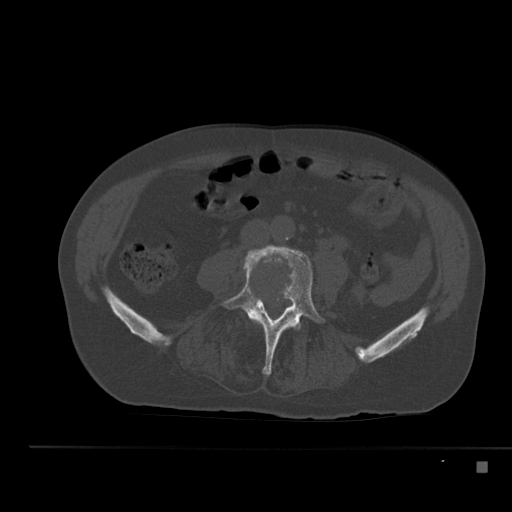
CT including the spine, one axial slice; position 143 of 517 along the scan axis; reconstruction kernel Br40s; 120 kVp; bone window (W 1800 / L 400 HU); 1.5 mm slice thickness; 512 × 512 image matrix, field of view 408 × 408 mm. Patient: male, 70 years. From the clinical record (not read from this slice): primary cancer: renal.
Annotated regions visible in this slice (semi-automatic segmentation, software-assisted and operator-edited):
- L4 vertebra: bounding box <220,245,325,376> (left, top, right, bottom; pixels)